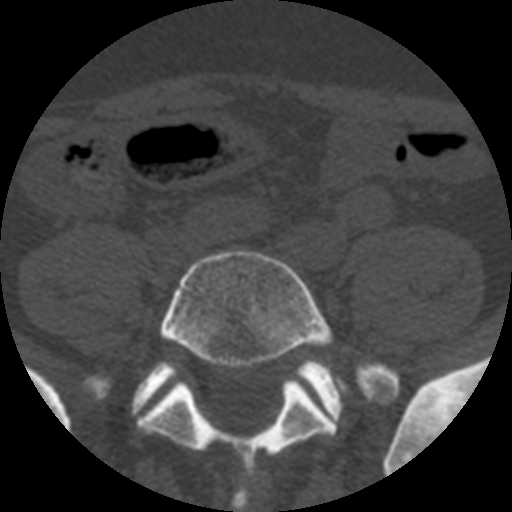
CT including the spine, one axial slice; slice 60 of 508 in the series (ordered by position); 120 kVp; bone window (W 1800 / L 400 HU); 1.25 mm slice thickness; 512 × 512 image matrix, field of view 160 × 160 mm. Patient age 57 years. Case-level facts recorded for this patient, not image findings: primary cancer: prostate.
Annotated regions visible in this slice (semi-automatic segmentation, software-assisted and operator-edited):
- L5 vertebra: box from (x=137, y=250) to (x=394, y=480) px